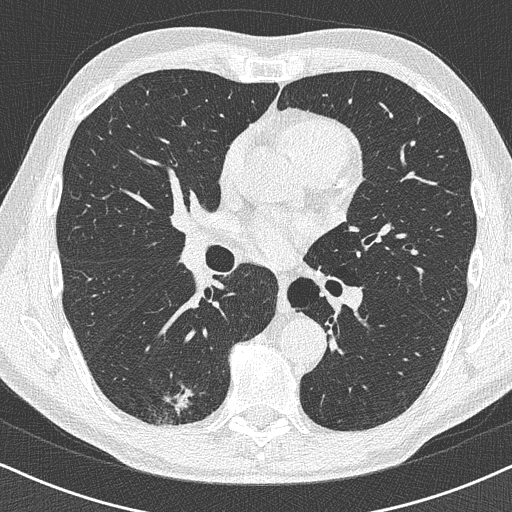
Low-dose screening chest CT, one axial slice; slice 234 of 438 in the series (ordered by position); lung window (W 1500 / L -600 HU); 1 mm slice thickness; 512 × 512 image matrix.
Annotated regions visible in this slice (manually delineated by an expert):
- lesion 1 (tumor, lower lobe of right lung): box from (x=174, y=389) to (x=190, y=411) px